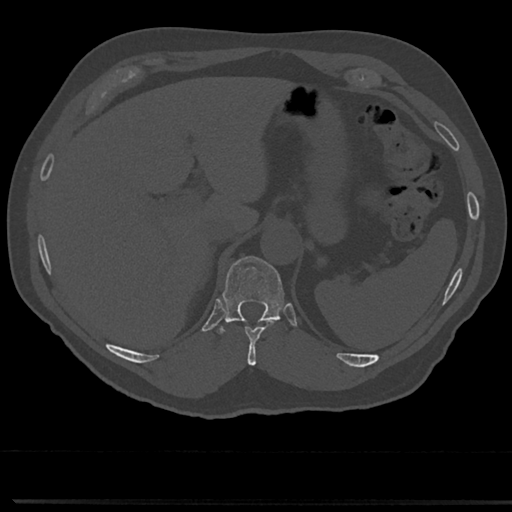
CT including the spine, one axial slice; slice 224 of 817 in the series (ordered by position); reconstruction kernel Br40s/3; bone window (W 1800 / L 400 HU); 0.5 mm slice thickness; 512 × 512 image matrix, field of view 355 × 355 mm. Male patient, age 61 years. From the clinical record (not read from this slice): primary cancer: prostate.
Structures marked on this image (semi-automatically segmented with operator editing):
- T10 vertebra: bounding box <233,319,278,365> (left, top, right, bottom; pixels)
- T11 vertebra: <223,256,284,321>